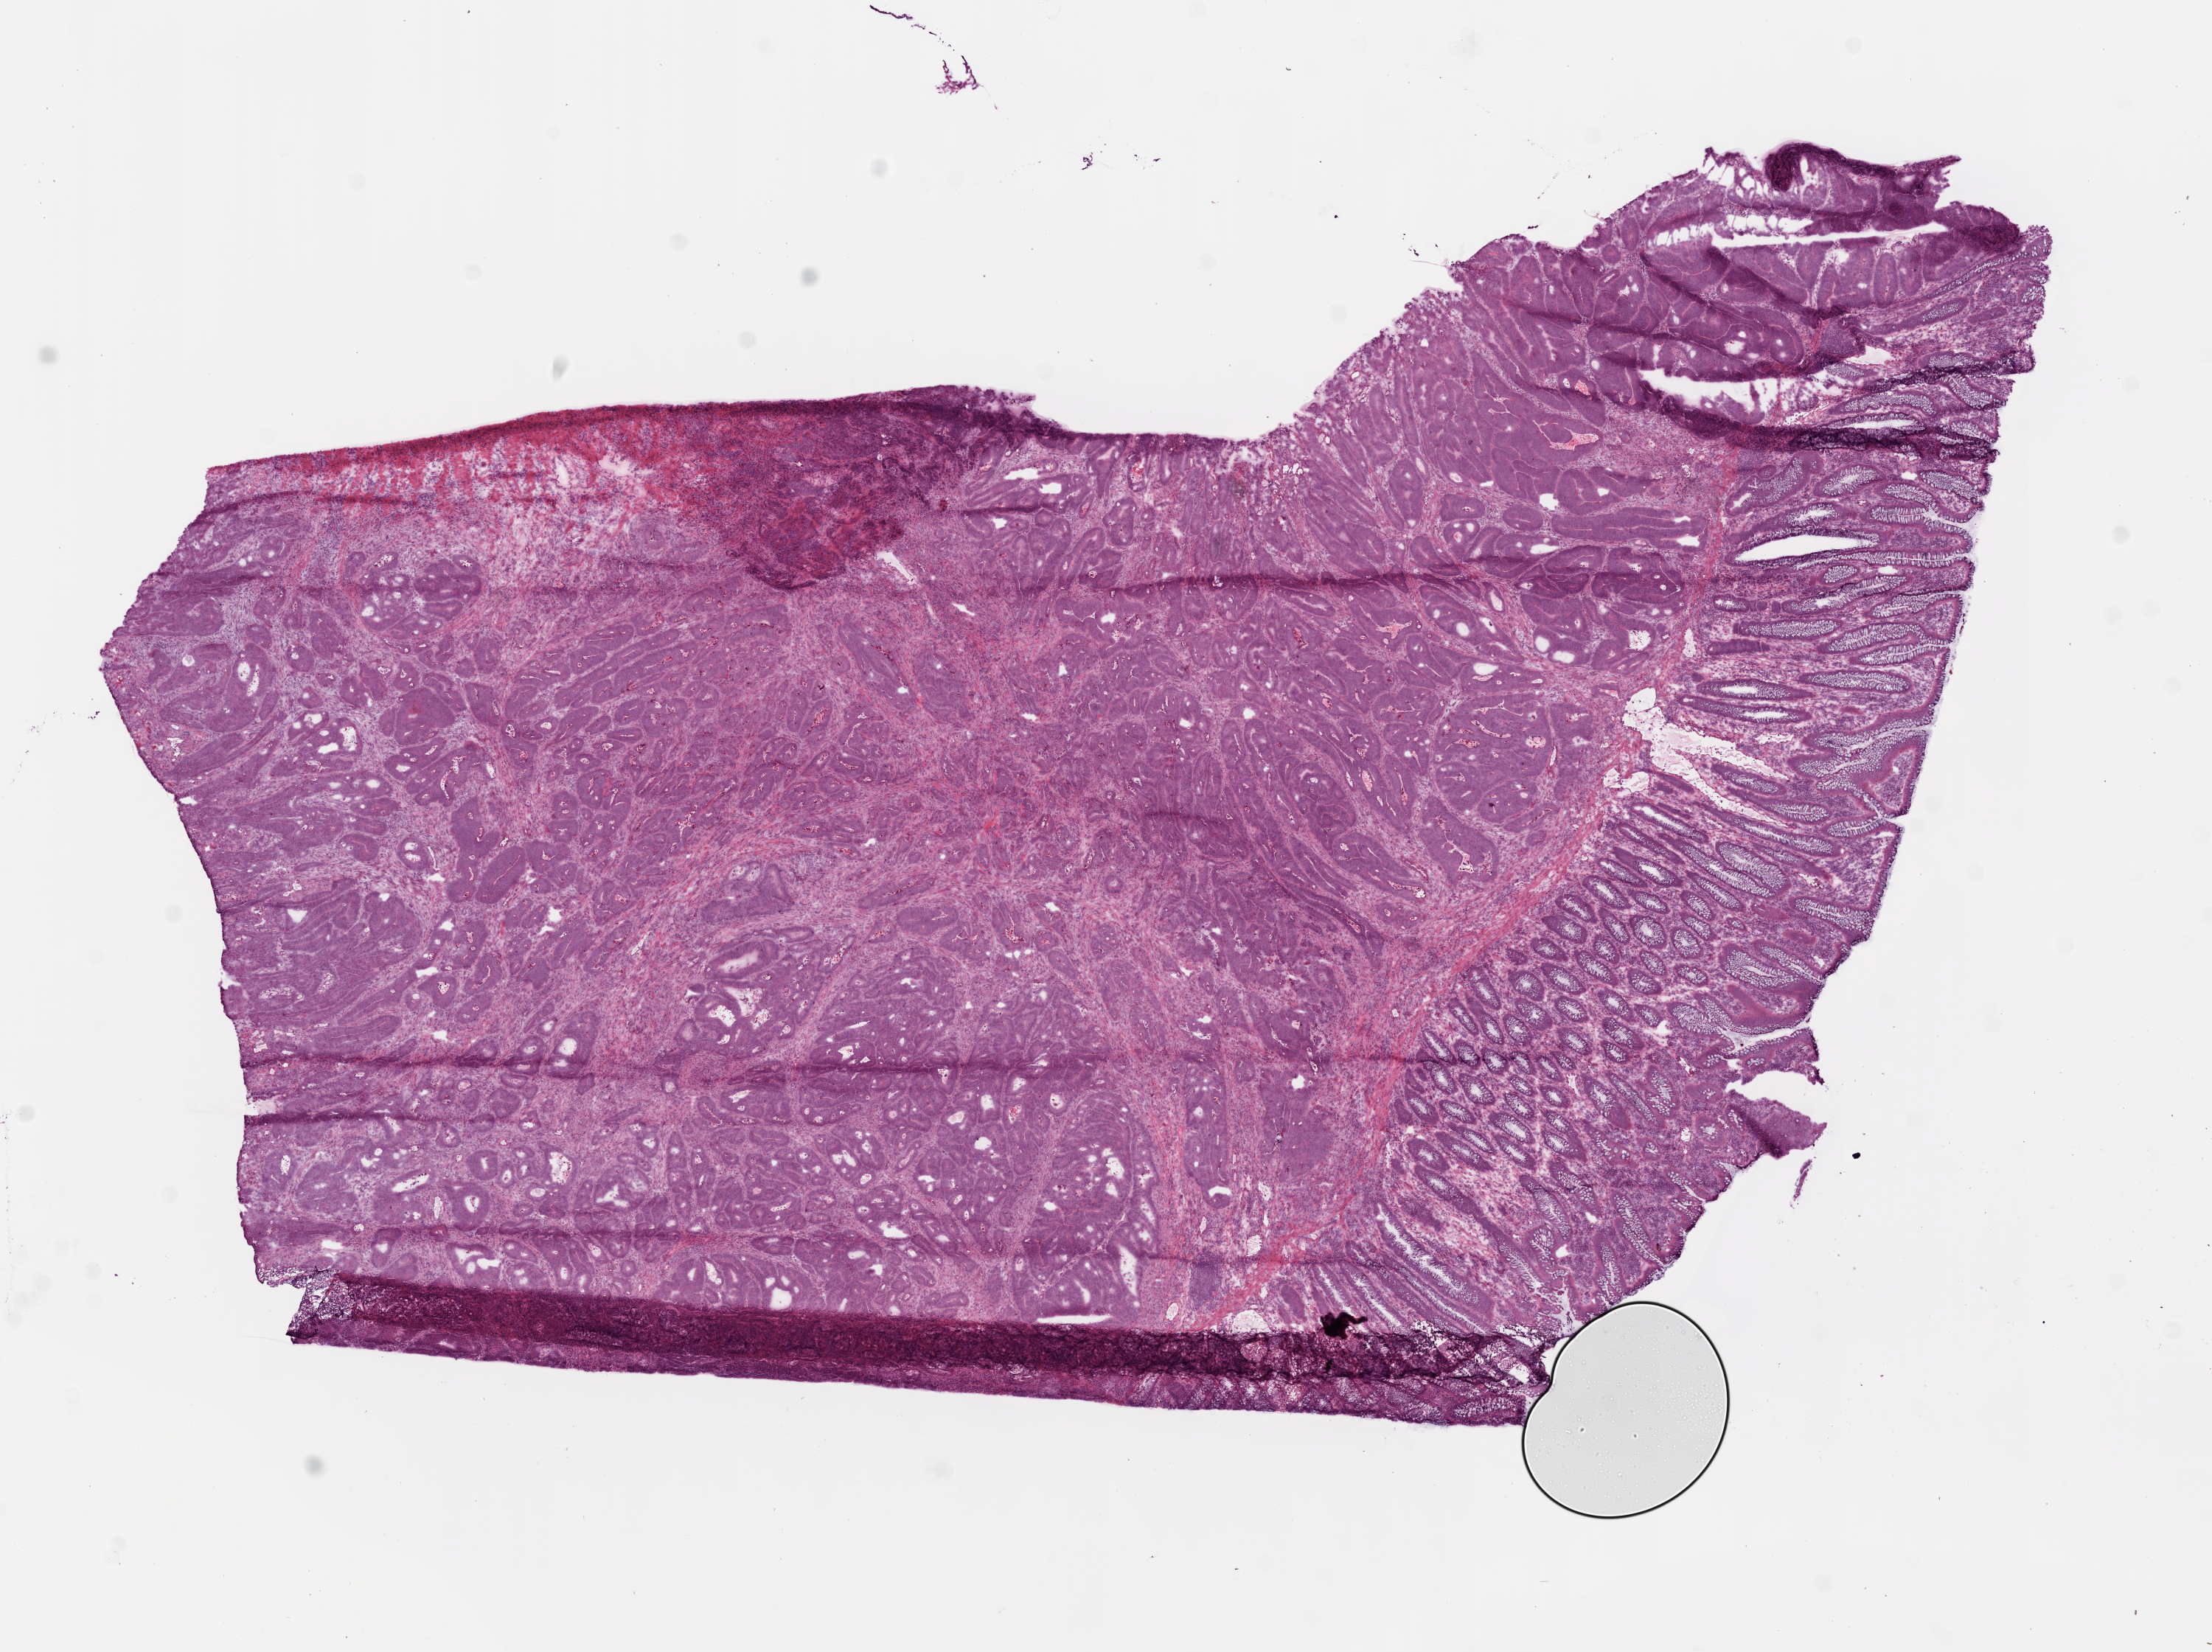
Whole-slide histology image, H&E — shown as a low-resolution overview of the whole scanned area (about 12.0 x 9.0 mm), frozen section, colon, primary tumour sample. Patient: male, age at initial diagnosis 69 years. Slide review estimates, as recorded: tumour cells 60%, tumour nuclei 70%, normal cells 20%, stromal cells 12%, necrosis 8%.
Diagnosis: Adenocarcinoma, NOS. Lymph nodes positive (case pathology): 0 of 24 examined. TNM: T3 N0 M0. AJCC pathologic stage: II (5th edition).